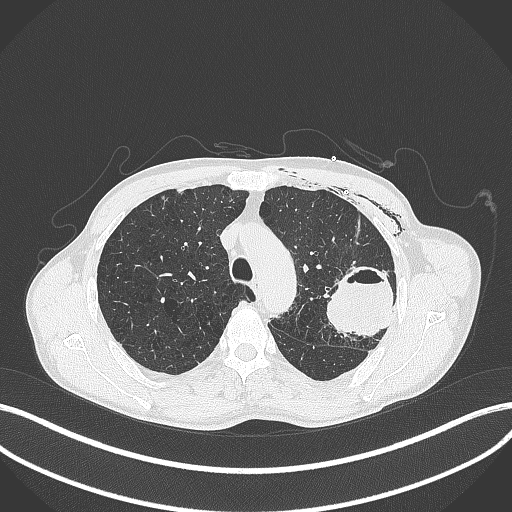
Chest CT, one axial slice; position 300 of 457 along the scan axis; 120 kVp; lung window (W 1500 / L -600 HU); 1 mm slice thickness; 512 × 512 image matrix, field of view 400 × 400 mm. Patient: male, 58 years. From the clinical record (not read from this slice): clinical TNM (as recorded): T3 N0 M0.
Structures marked on this image (bounding box drawn by a radiologist):
- lung tumour (recorded histology: adenocarcinoma): bounding box [x1, y1, x2, y2] px = [328, 264, 395, 339]